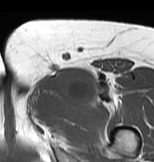
MRI of an extremity soft-tissue mass, one axial slice; position 44 of 83 along the scan axis; MR volume resampled by the dataset authors to the PET/CT grid (not the native acquisition matrix); 3.27 mm slice thickness; 154 × 162 image matrix, field of view 150 × 158 mm. Female patient. From the clinical record (not read from this slice): histological type: myxofibrosarcoma; grade: intermediate; site of the primary tumour: left thigh.
Structures marked on this image (expert contour drawn on MRI and transferred to this co-registered scan by the dataset authors):
- gross tumour volume including surrounding oedema: bounding box [x1, y1, x2, y2] px = [26, 68, 125, 119]
- gross tumour volume (mass): [49, 68, 93, 101]